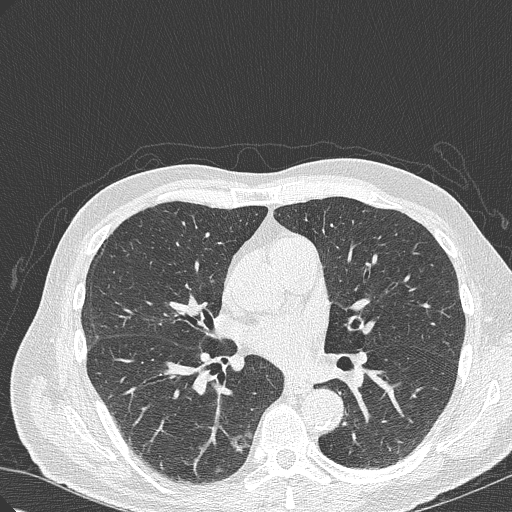
Axial slice from a low-dose chest CT screening exam, baseline annual screen, lung window (W 1500 / L -600 HU), 1 mm slice thickness, 512 × 512 image matrix. Male participant, aged 70 years at enrolment. Current smoker at enrolment.
Lesion marked by an expert reader, bounding box <197,420,260,482> (left, top, right, bottom; pixels). The screening reader recorded 4 non-calcified nodules or masses ≥4 mm on this exam (right lower lobe, right lower lobe, right upper lobe, right lower lobe); which of them this box marks is not recorded. Official screen result: positive, change unspecified: nodule(s) >= 4 mm or enlarging nodule(s), mass(es), or other non-specific abnormalities suspicious for lung cancer. Later outcome: lung cancer diagnosed 978 days after this screen (after the third annual screen) — bronchiolo-alveolar adenocarcinoma, NOS, right lower lobe, poorly differentiated (G3), stage IB (AJCC 6th edition), 30 mm at pathology.